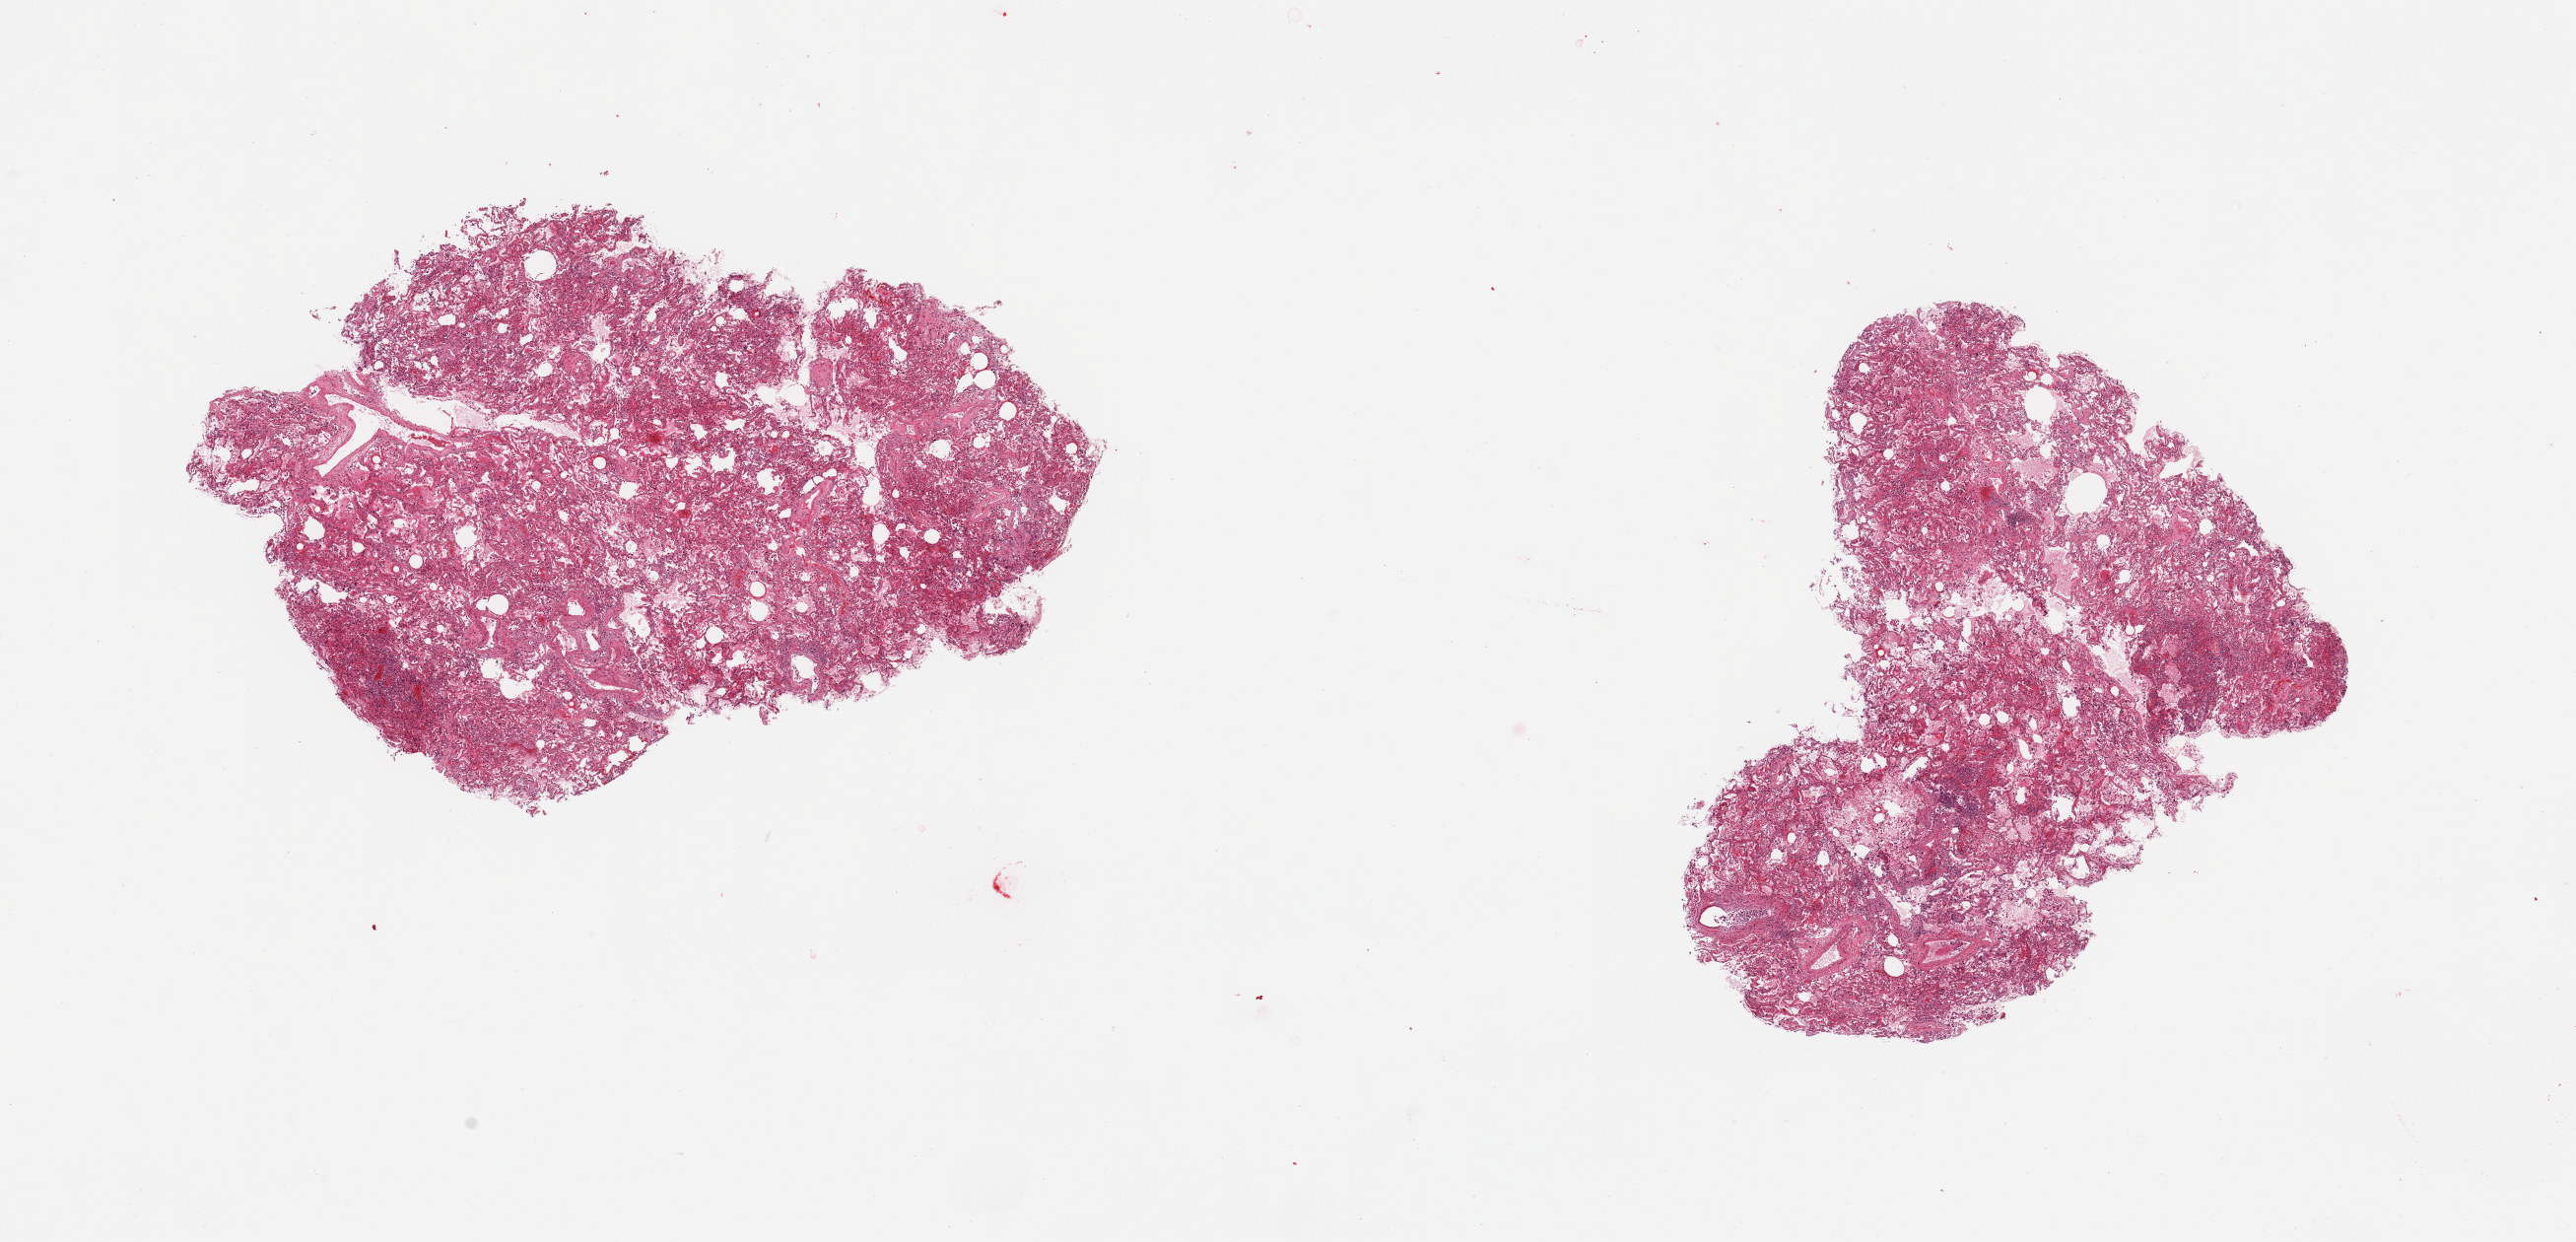
Digitized hematoxylin and eosin (H&E)-stained section — low-resolution overview of the scanned area, about 20.7 x 10.0 mm (from a 20x scan), PAXgene-fixed, paraffin-embedded tissue, sampled site (target tissue): lung, tissue donor sample. Donor: female.
* reviewer comment on this tissue sample: 2 pieces; patchy pneumonia and congestion